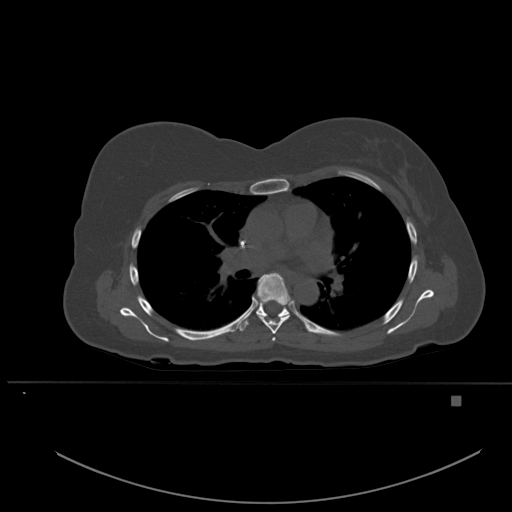
CT including the spine, one axial slice; position 359 of 651 along the scan axis; bone window (W 1800 / L 400 HU); 512 × 512 image matrix, field of view 443 × 443 mm. Female patient, age 49 years. From the clinical record (not read from this slice): primary cancer: breast; vertebrae with lytic lesions (as recorded): L3, T12, L4.
Annotated regions visible in this slice (semi-automatically segmented with operator editing):
- T4 vertebra: bounding box [x1, y1, x2, y2] px = [272, 337, 276, 341]
- T5 vertebra: [256, 273, 291, 334]
- T6 vertebra: [239, 301, 290, 331]